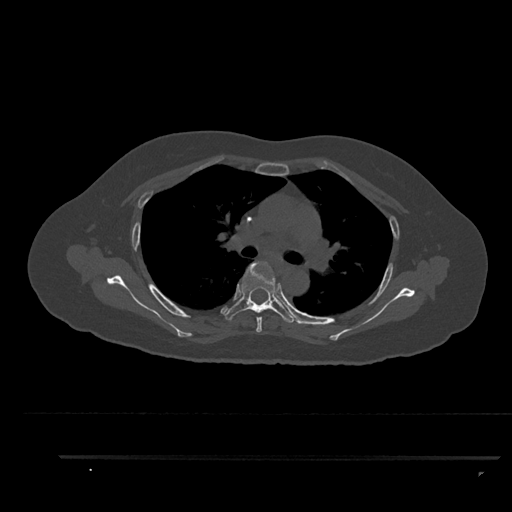
CT including the spine, one axial slice; slice 614 of 797 in the series (ordered by position); reconstruction kernel Br40s/3; 120 kVp; bone window (W 1800 / L 400 HU); 0.5 mm slice thickness; 512 × 512 image matrix, field of view 408 × 408 mm. Female patient, age 44 years. Case-level facts recorded for this patient, not image findings: primary cancer: renal.
Annotated regions visible in this slice (semi-automatically segmented with operator editing):
- T4 vertebra: bounding box <256,317,262,333> (left, top, right, bottom; pixels)
- T5 vertebra: <220,261,296,323>